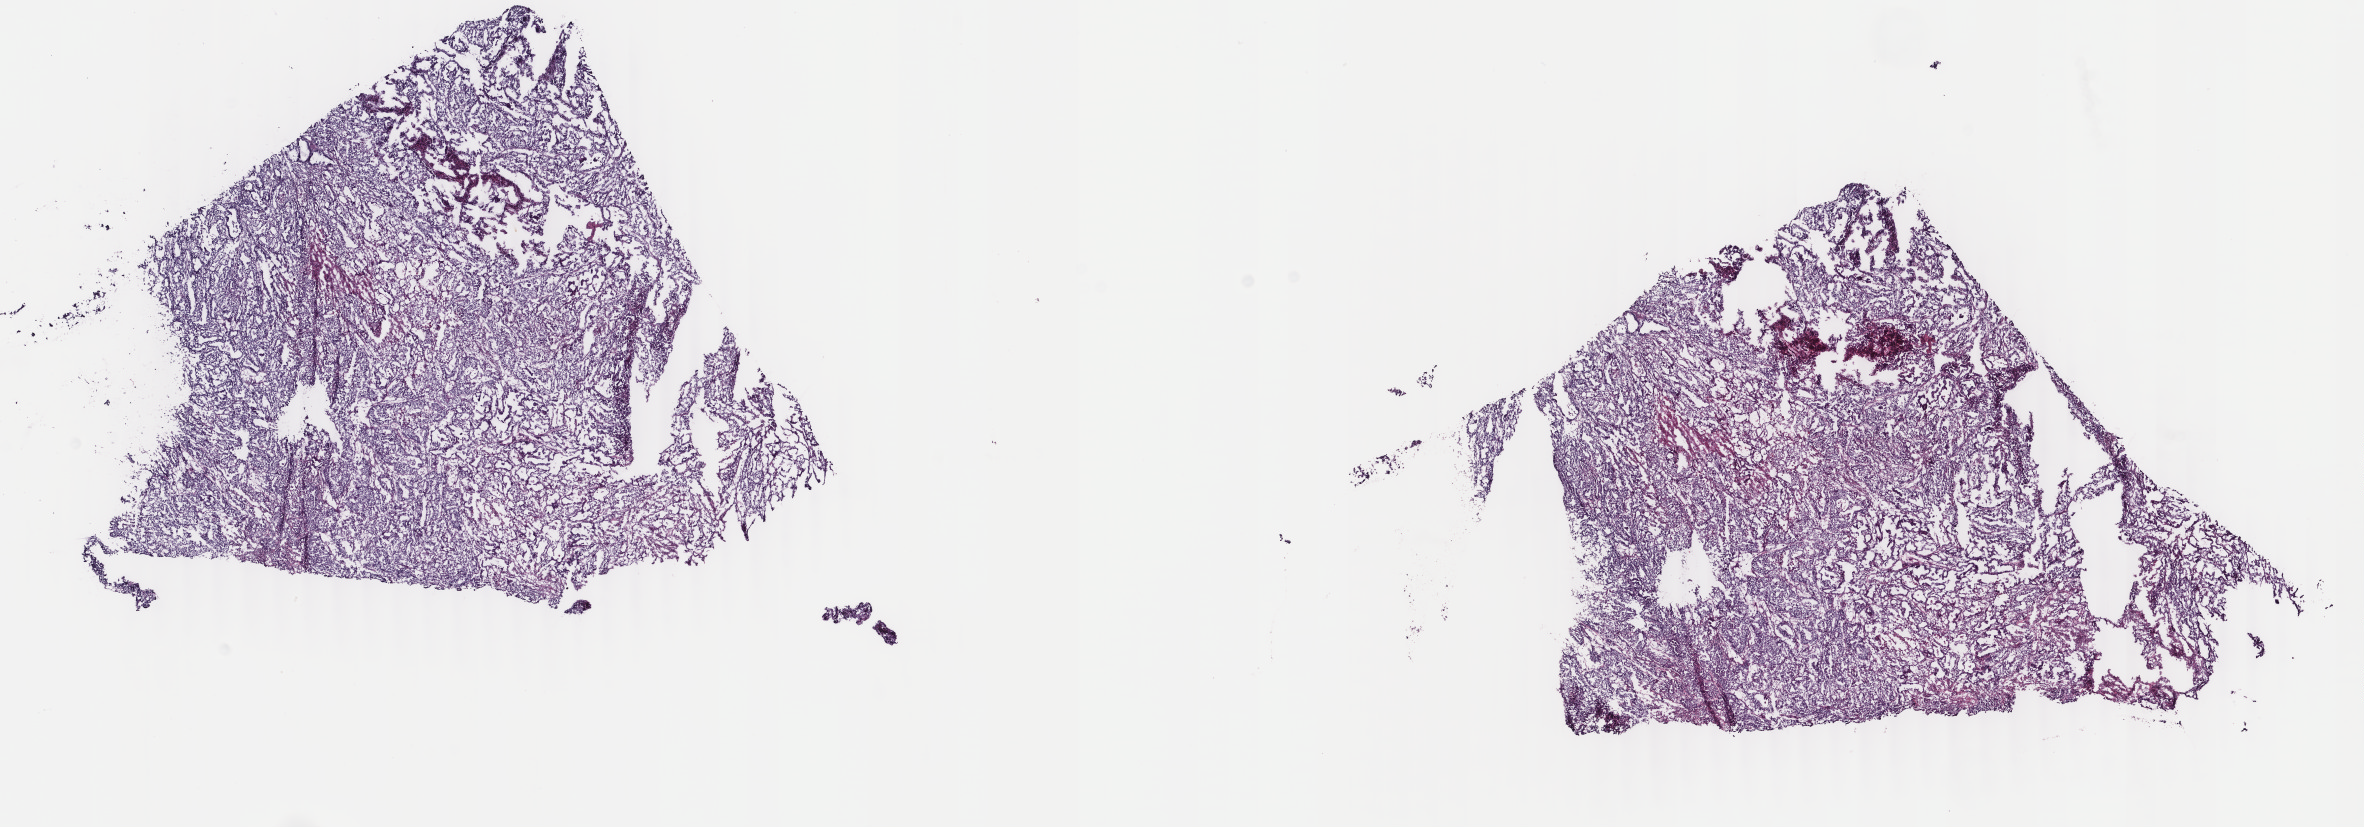
Whole-slide histology image, Hematoxylin and eosin (H&E) stained, whole scanned area (about 18.8 x 6.6 mm, slide scanned at 40x) shown as a low-resolution overview, frozen section, primary tumour sample from the uterus. Female patient; age at initial diagnosis 71 years. Histologic grade: G3 (poorly differentiated). Composition of this section per pathologist review: tumour cells 80%, tumour nuclei 80%, normal cells 0%, stromal cells 15%, necrosis 5%. Inflammatory infiltration, as recorded: lymphocyte infiltration 40%, monocyte infiltration 20%, neutrophil infiltration 20%.
Histologic diagnosis: Endometrioid adenocarcinoma, NOS (endometrium). FIGO stage: IB.